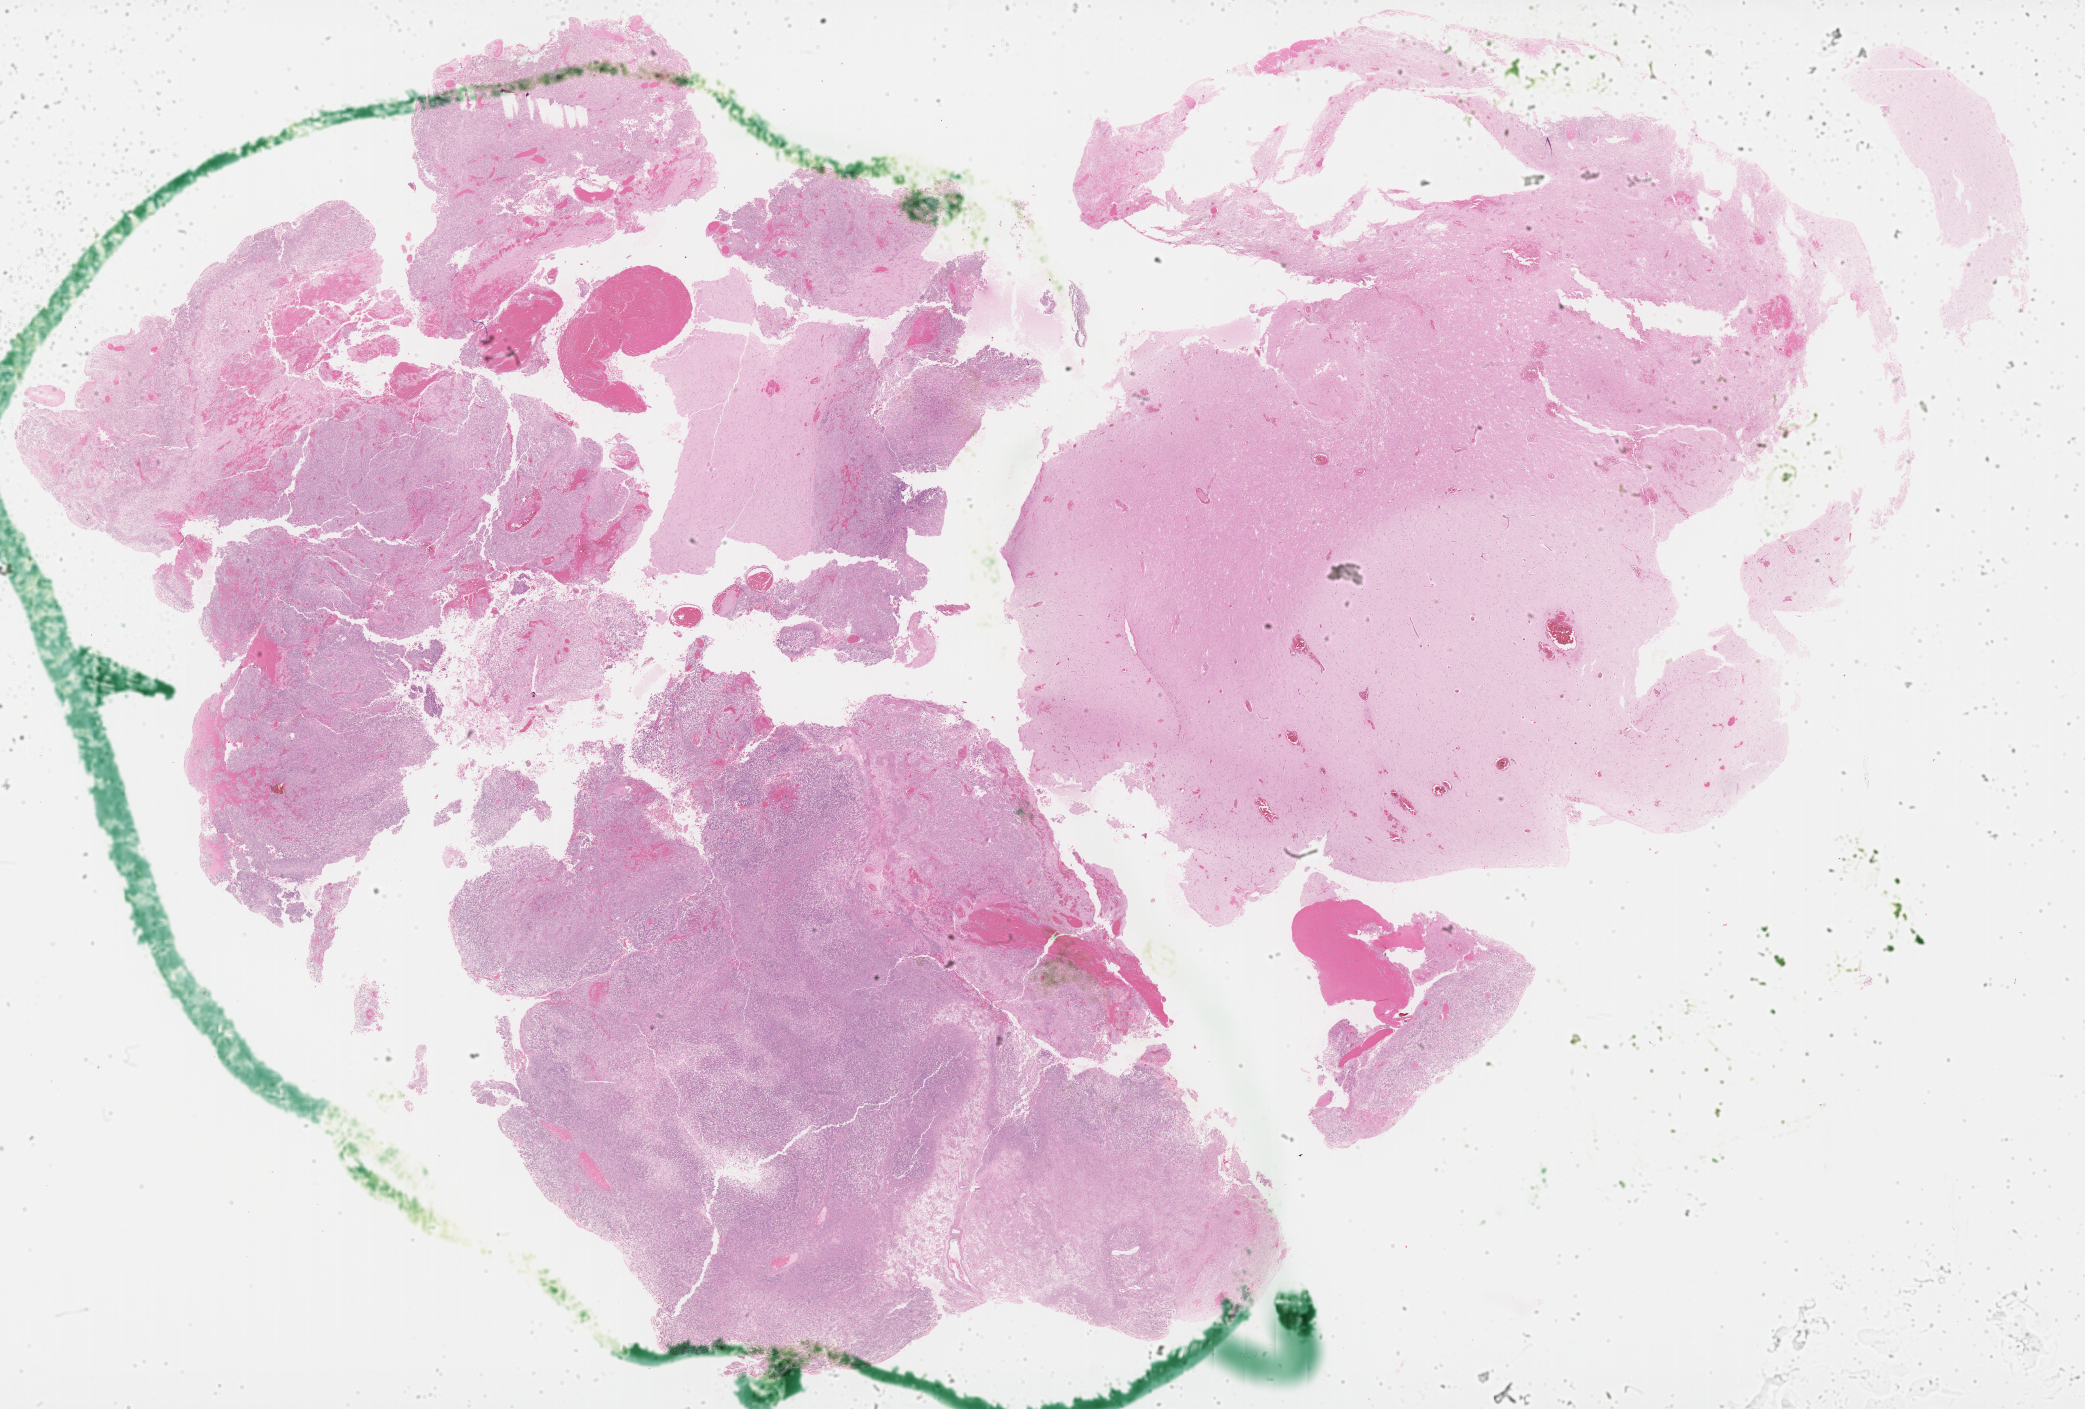
Digitized H&E tissue section (whole slide), whole scanned area (about 33.8 x 22.8 mm, slide scanned at 40x) shown as a low-resolution overview, FFPE section, sample: primary tumour, brain. Male, age 49 years at initial diagnosis.
• diagnosis: Glioblastoma